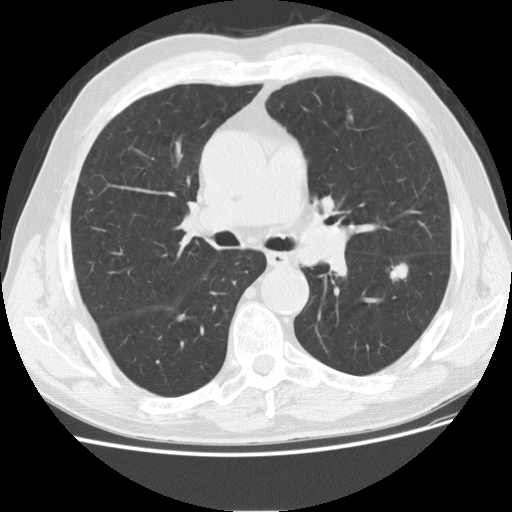
Low-dose screening chest CT, one axial slice. Position 110 of 175 along the scan axis. 120 kVp. Lung window (W 1500 / L -600 HU). 2.5 mm slice thickness. 512 × 512 image matrix, field of view 360 × 360 mm.
Outlined on this slice (outlined manually by an expert reader):
- lesion 1 (tumor, lower lobe of left lung): bounding box [x1, y1, x2, y2] px = [390, 263, 408, 281]